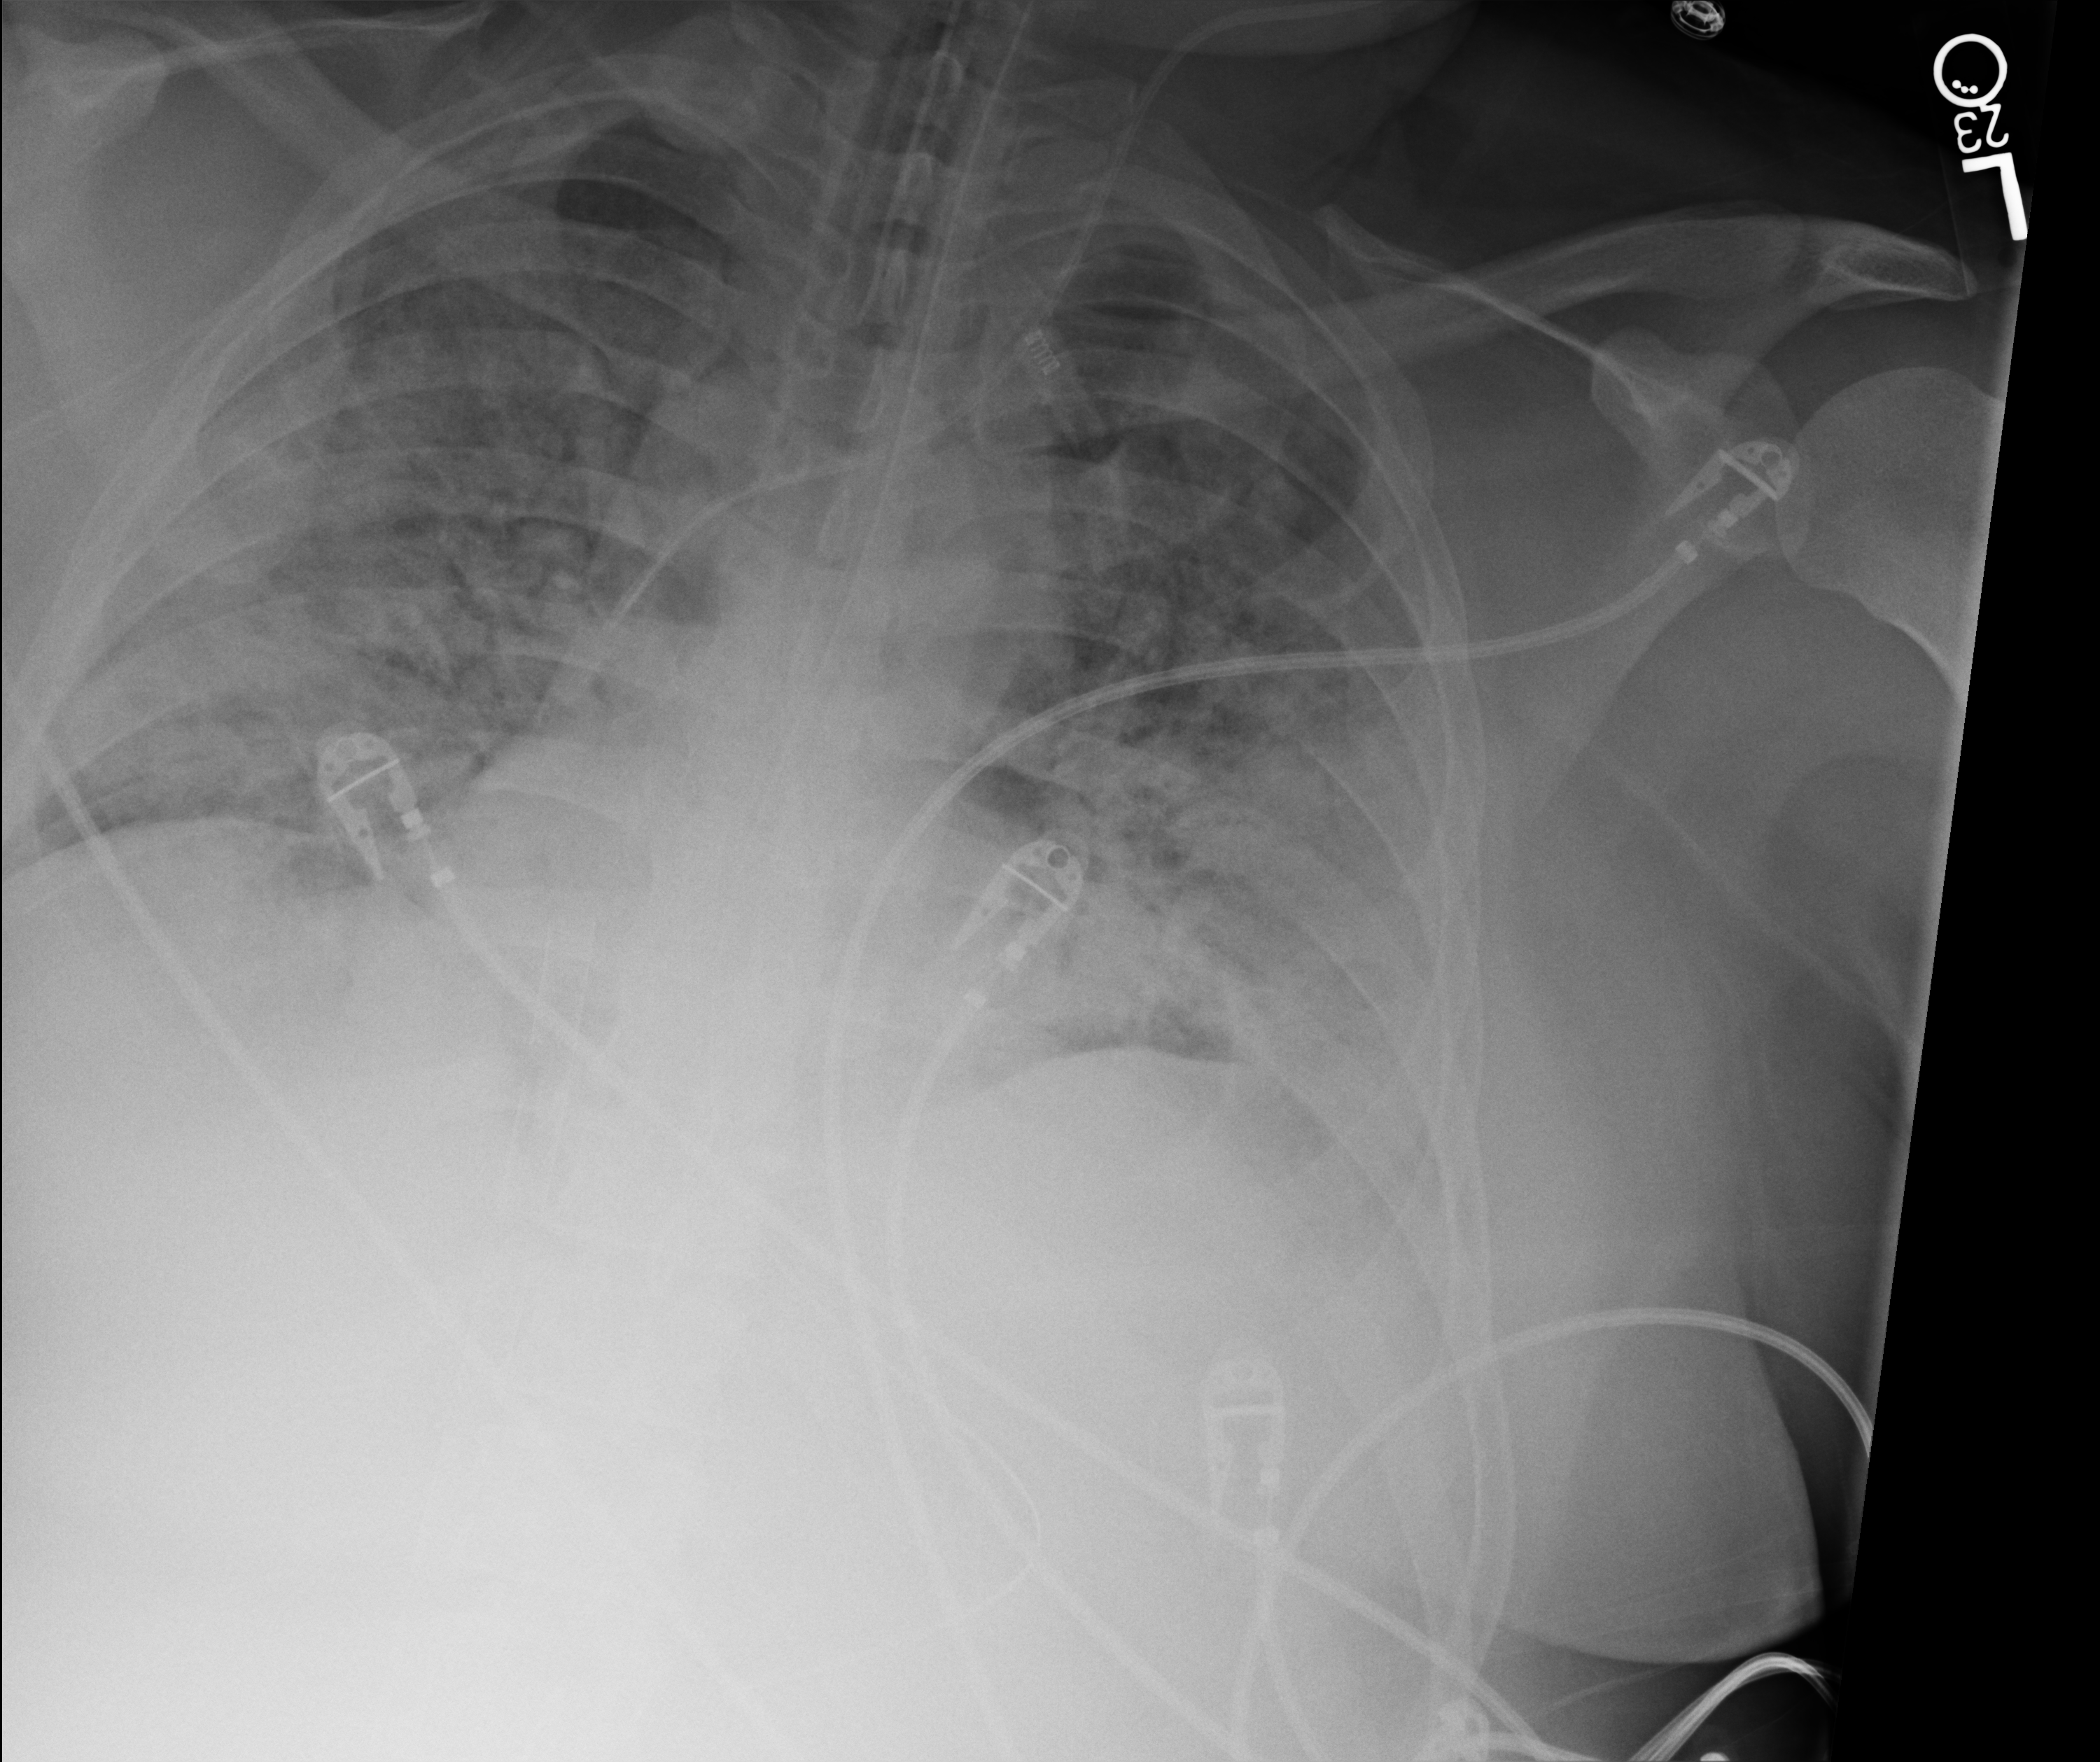
Bedside chest radiograph (computed radiography); anteroposterior (AP) projection. Adult patient hospitalised with COVID-19, age 18–59 years.
Hospital-stay facts (about this admission, not read from this image; timing relative to this image not recorded): length of hospital stay: 15 days; admitted to intensive care during this hospital stay: yes; COPD (admission record): no.